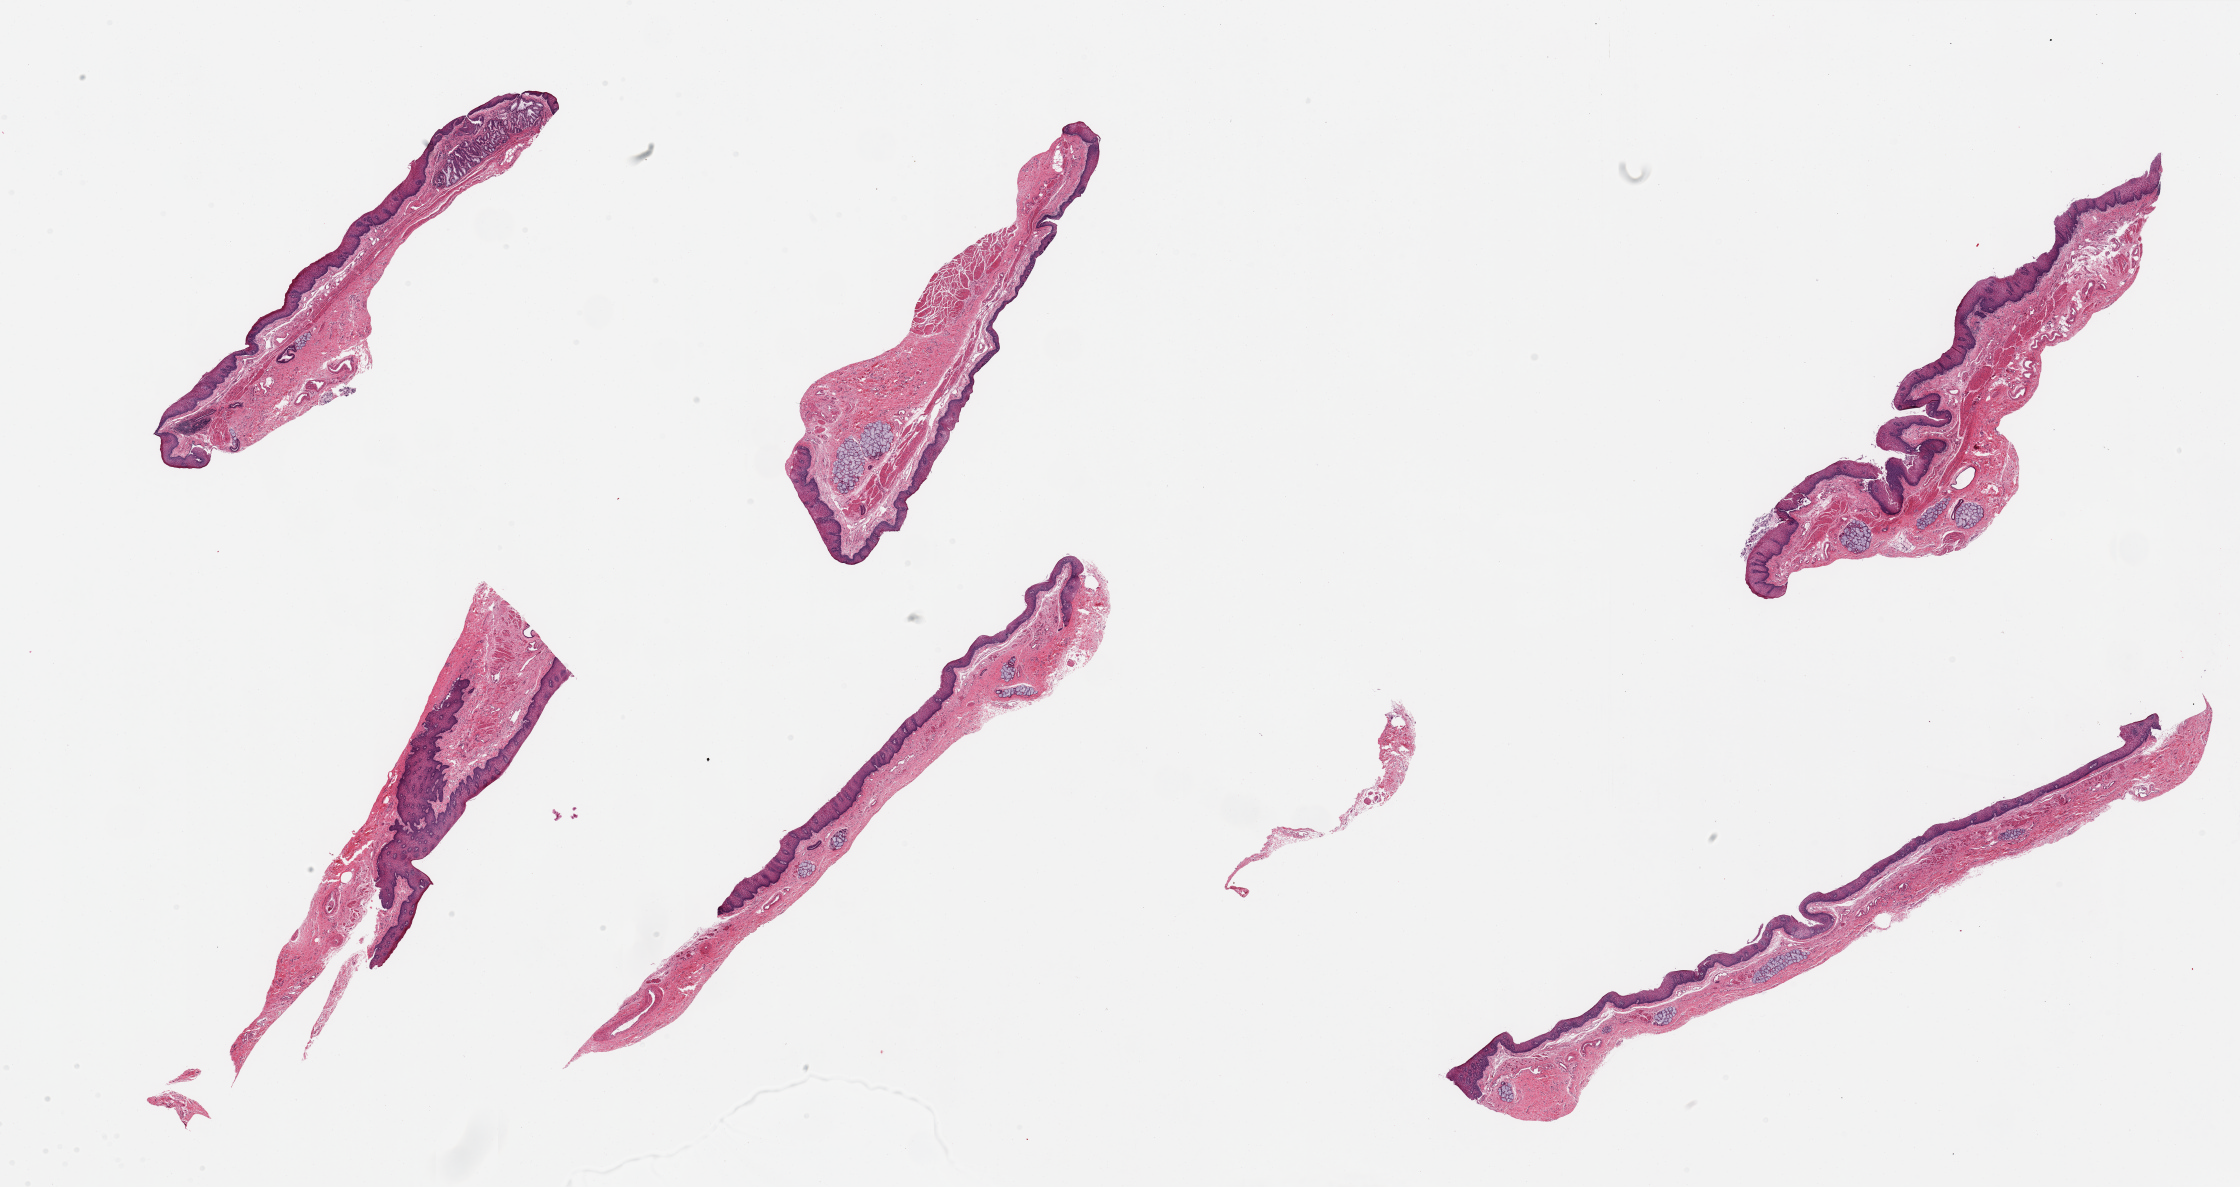
Whole-slide image, hematoxylin and eosin (H&E) stain — shown as a low-resolution overview of the whole scanned area (about 35.4 x 18.8 mm); PAXgene-fixed paraffin-embedded (PFPE) section; section of esophageal mucous membrane (target tissue); tissue donor sample. Donor sex: female.
Pathologist's review note for this sample: 6 pieces, squamous mucosa is ~0.3mm, ~10-15% thickness; Submucosal mucus glands noted.